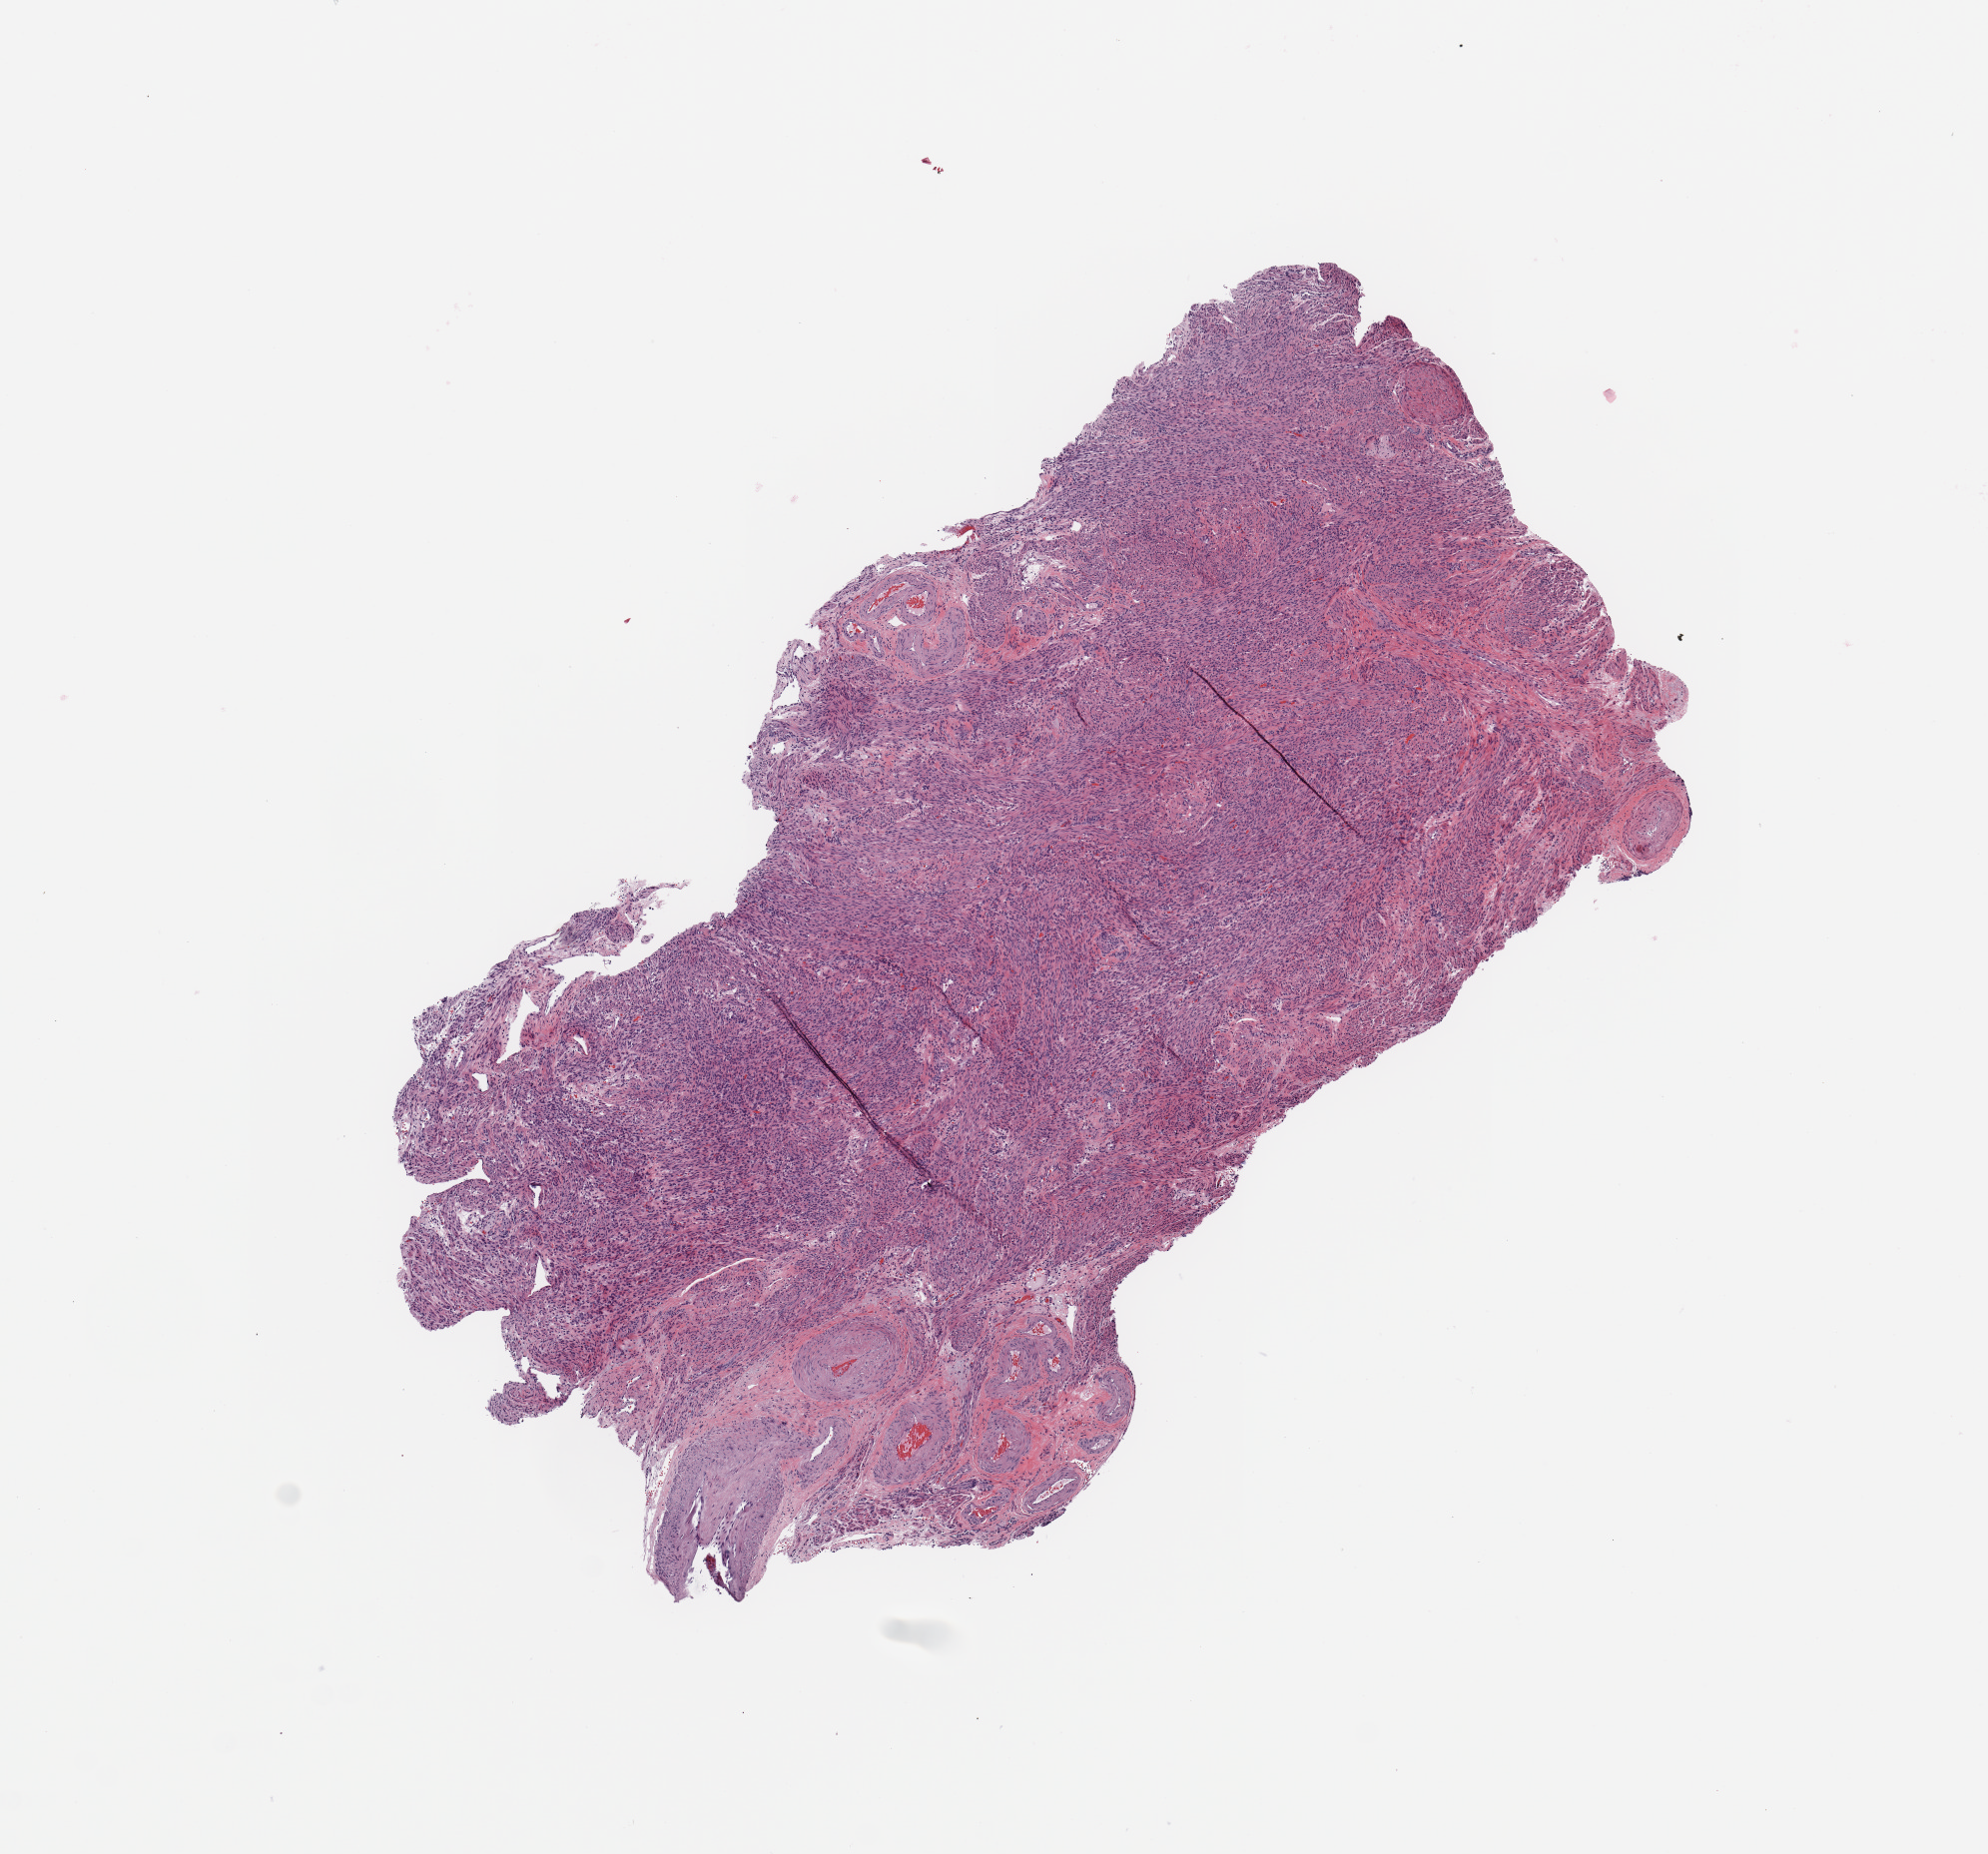
Digitized Hematoxylin and eosin (H&E) stained tissue section (whole slide) — shown as a low-resolution overview of the whole scanned area (about 7.9 x 7.3 mm, acquisition: 20x scan); uterus, normal (non-tumour) tissue. Patient: female, age 71 years.
This section: normal (non-tumour) tissue from the same patient. Patient diagnosis: Endometrioid adenocarcinoma, NOS.